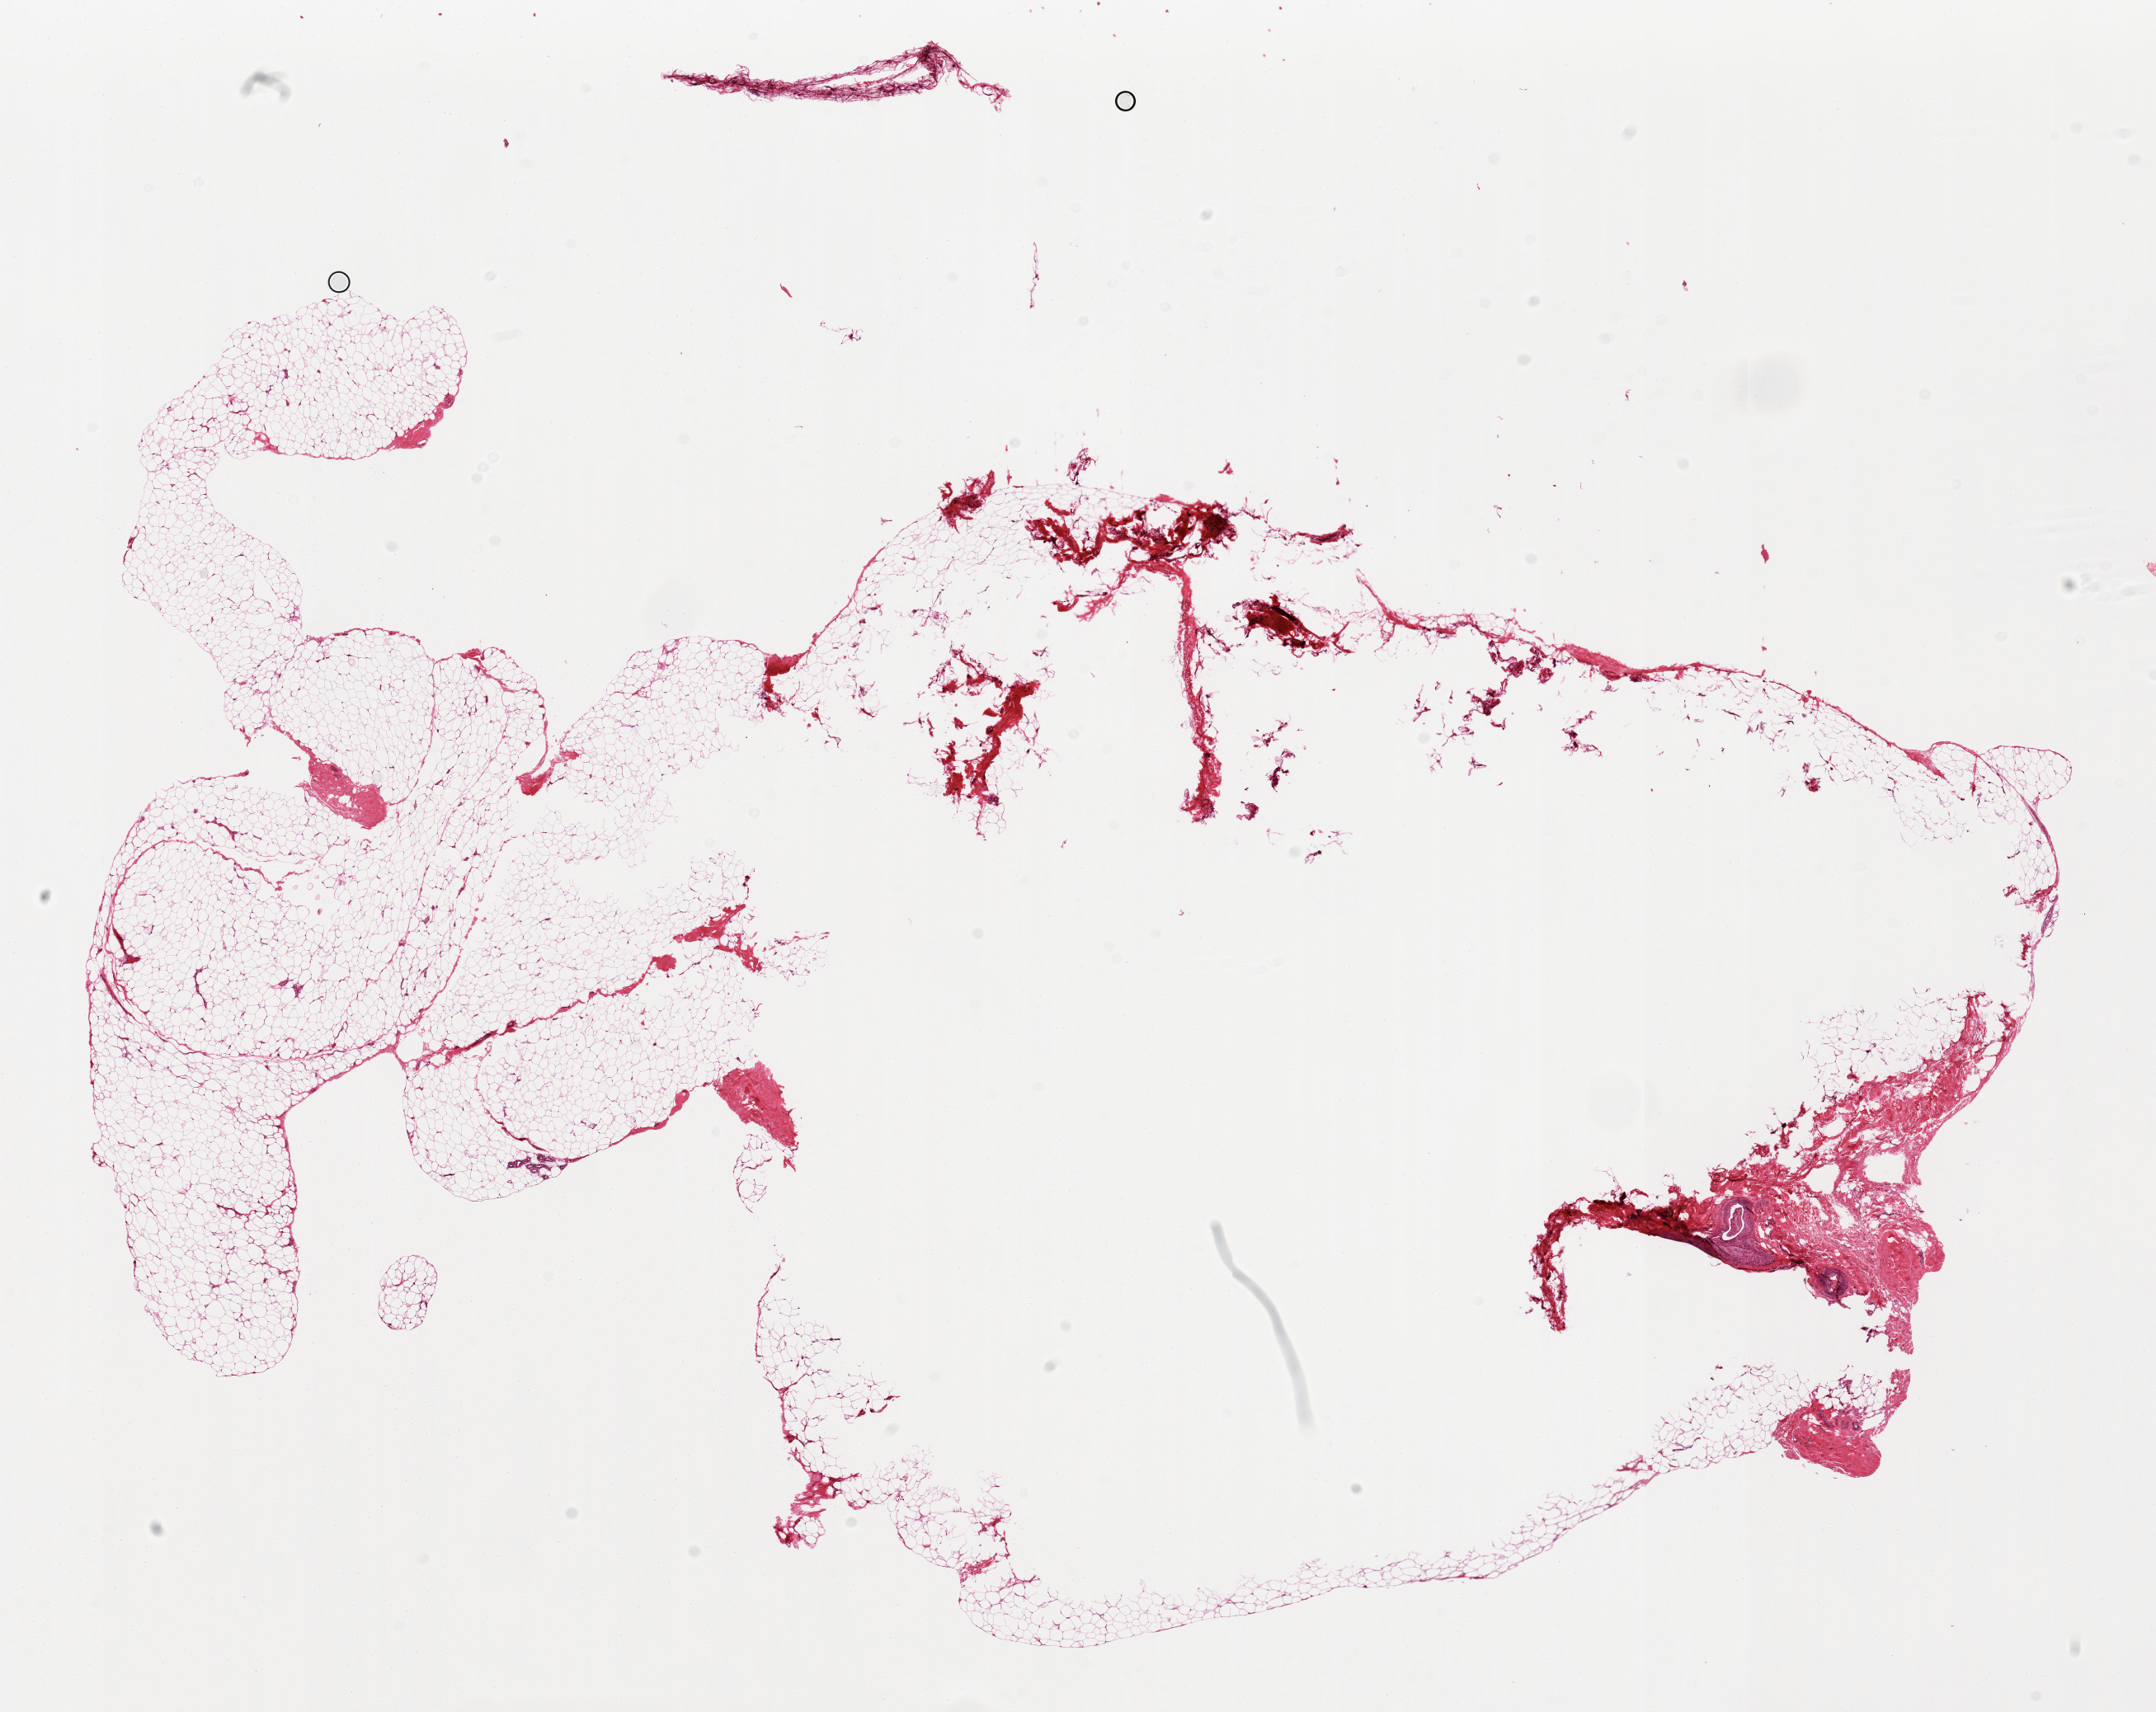
Haematoxylin and eosin whole-slide image, shown as a low-resolution overview of the whole scanned area (about 20.7 x 16.4 mm, from a 20x scan). PAXgene-fixed paraffin-embedded (PFPE) section. Sampled site (target tissue): adipose tissue. Tissue donor sample.
Review note (as recorded): 18x11mm. Central 80% is unfixed.